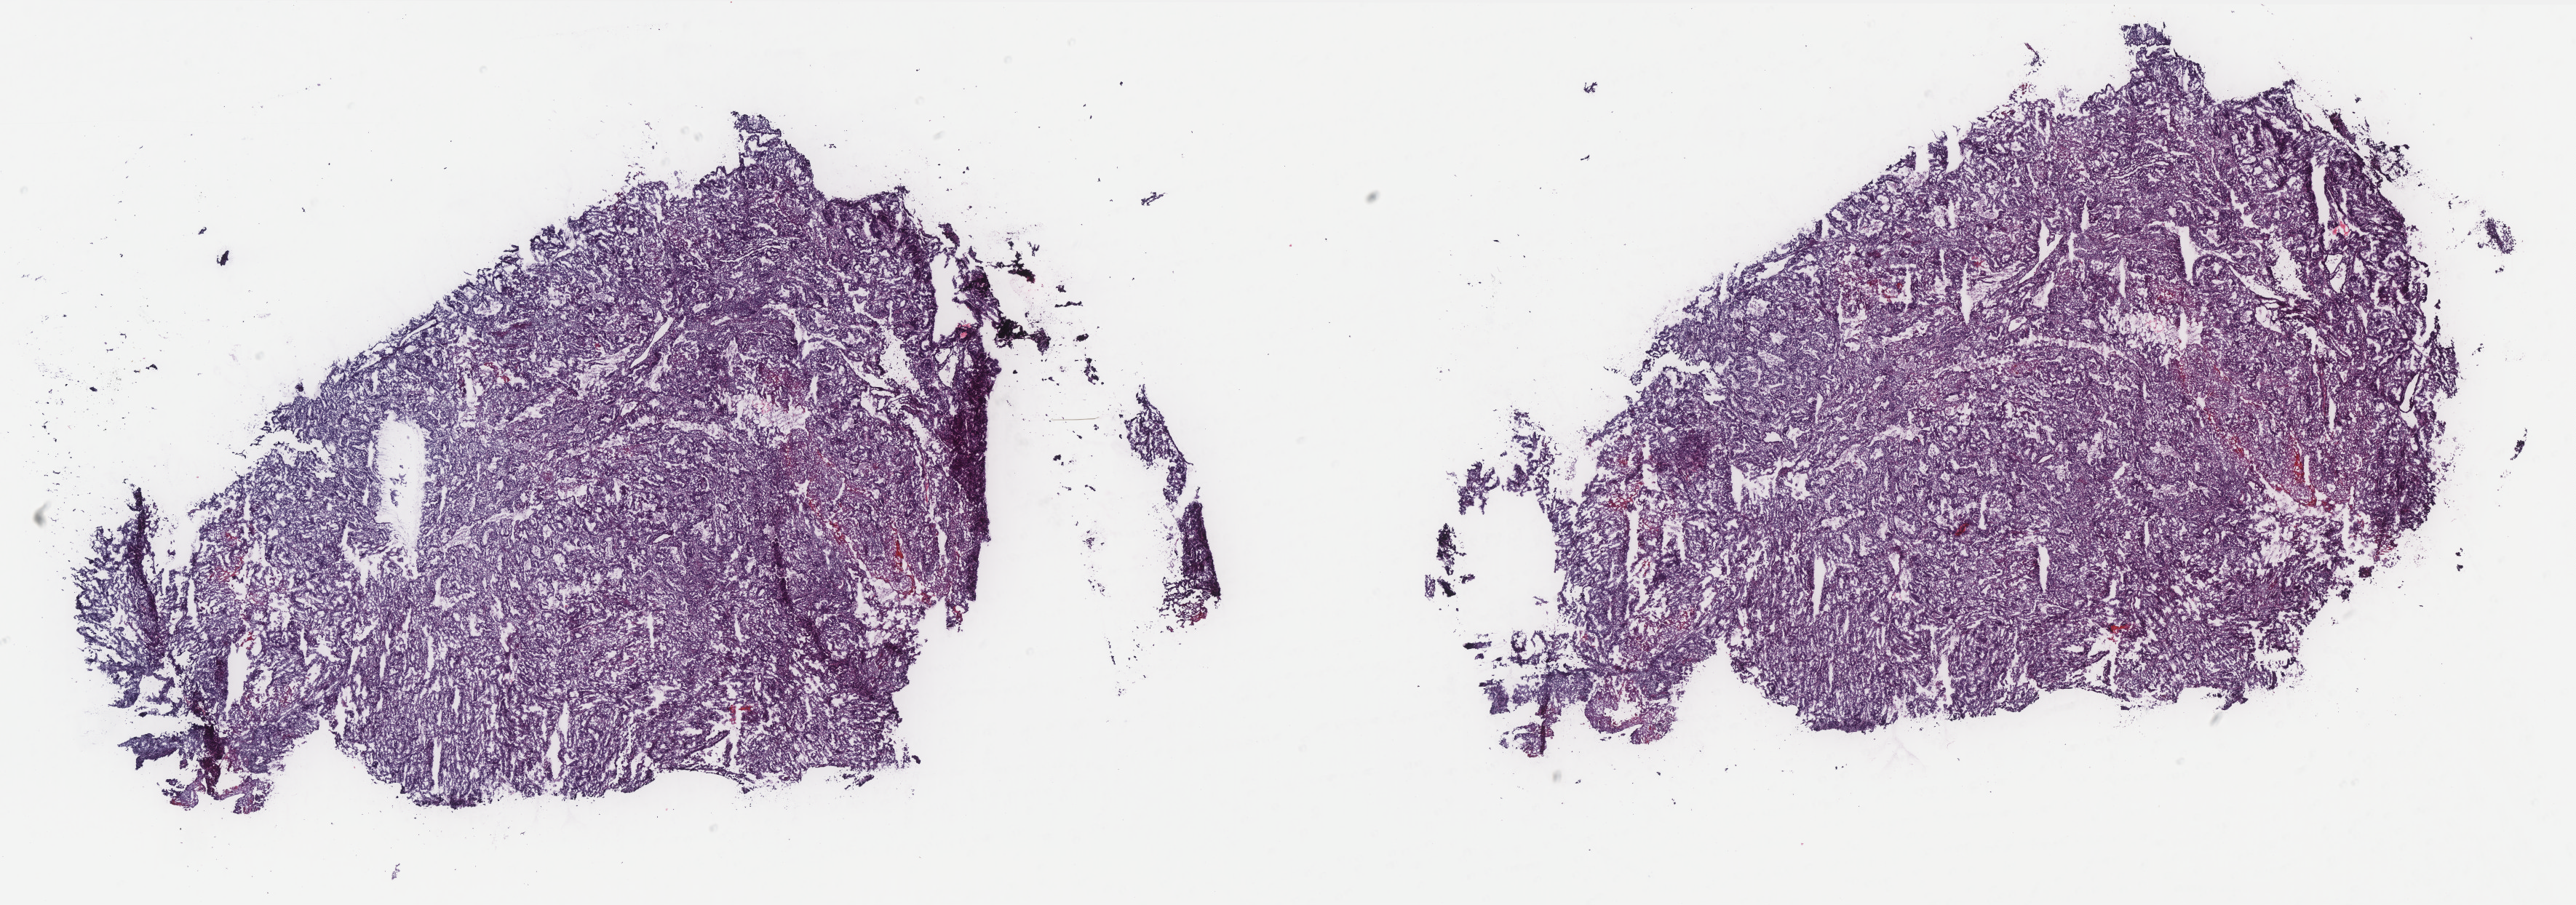
Whole-slide histology image, H&E, a low-resolution overview of the entire scanned area, about 28.4 x 10.0 mm (from a 40x scan). Frozen section. Primary tumour sample from the uterus. Patient: female, age at initial diagnosis 58 years. Histologic grade: G1 (well differentiated). Slide review estimates, as recorded: tumour cells 50%, tumour nuclei 50%, normal cells 10%, stromal cells 35%, necrosis 5%. Inflammatory infiltration, as recorded: lymphocyte infiltration 60%, monocyte infiltration 15%, neutrophil infiltration 20%.
Diagnosis: Endometrioid adenocarcinoma, NOS (endometrium). FIGO stage: IB.